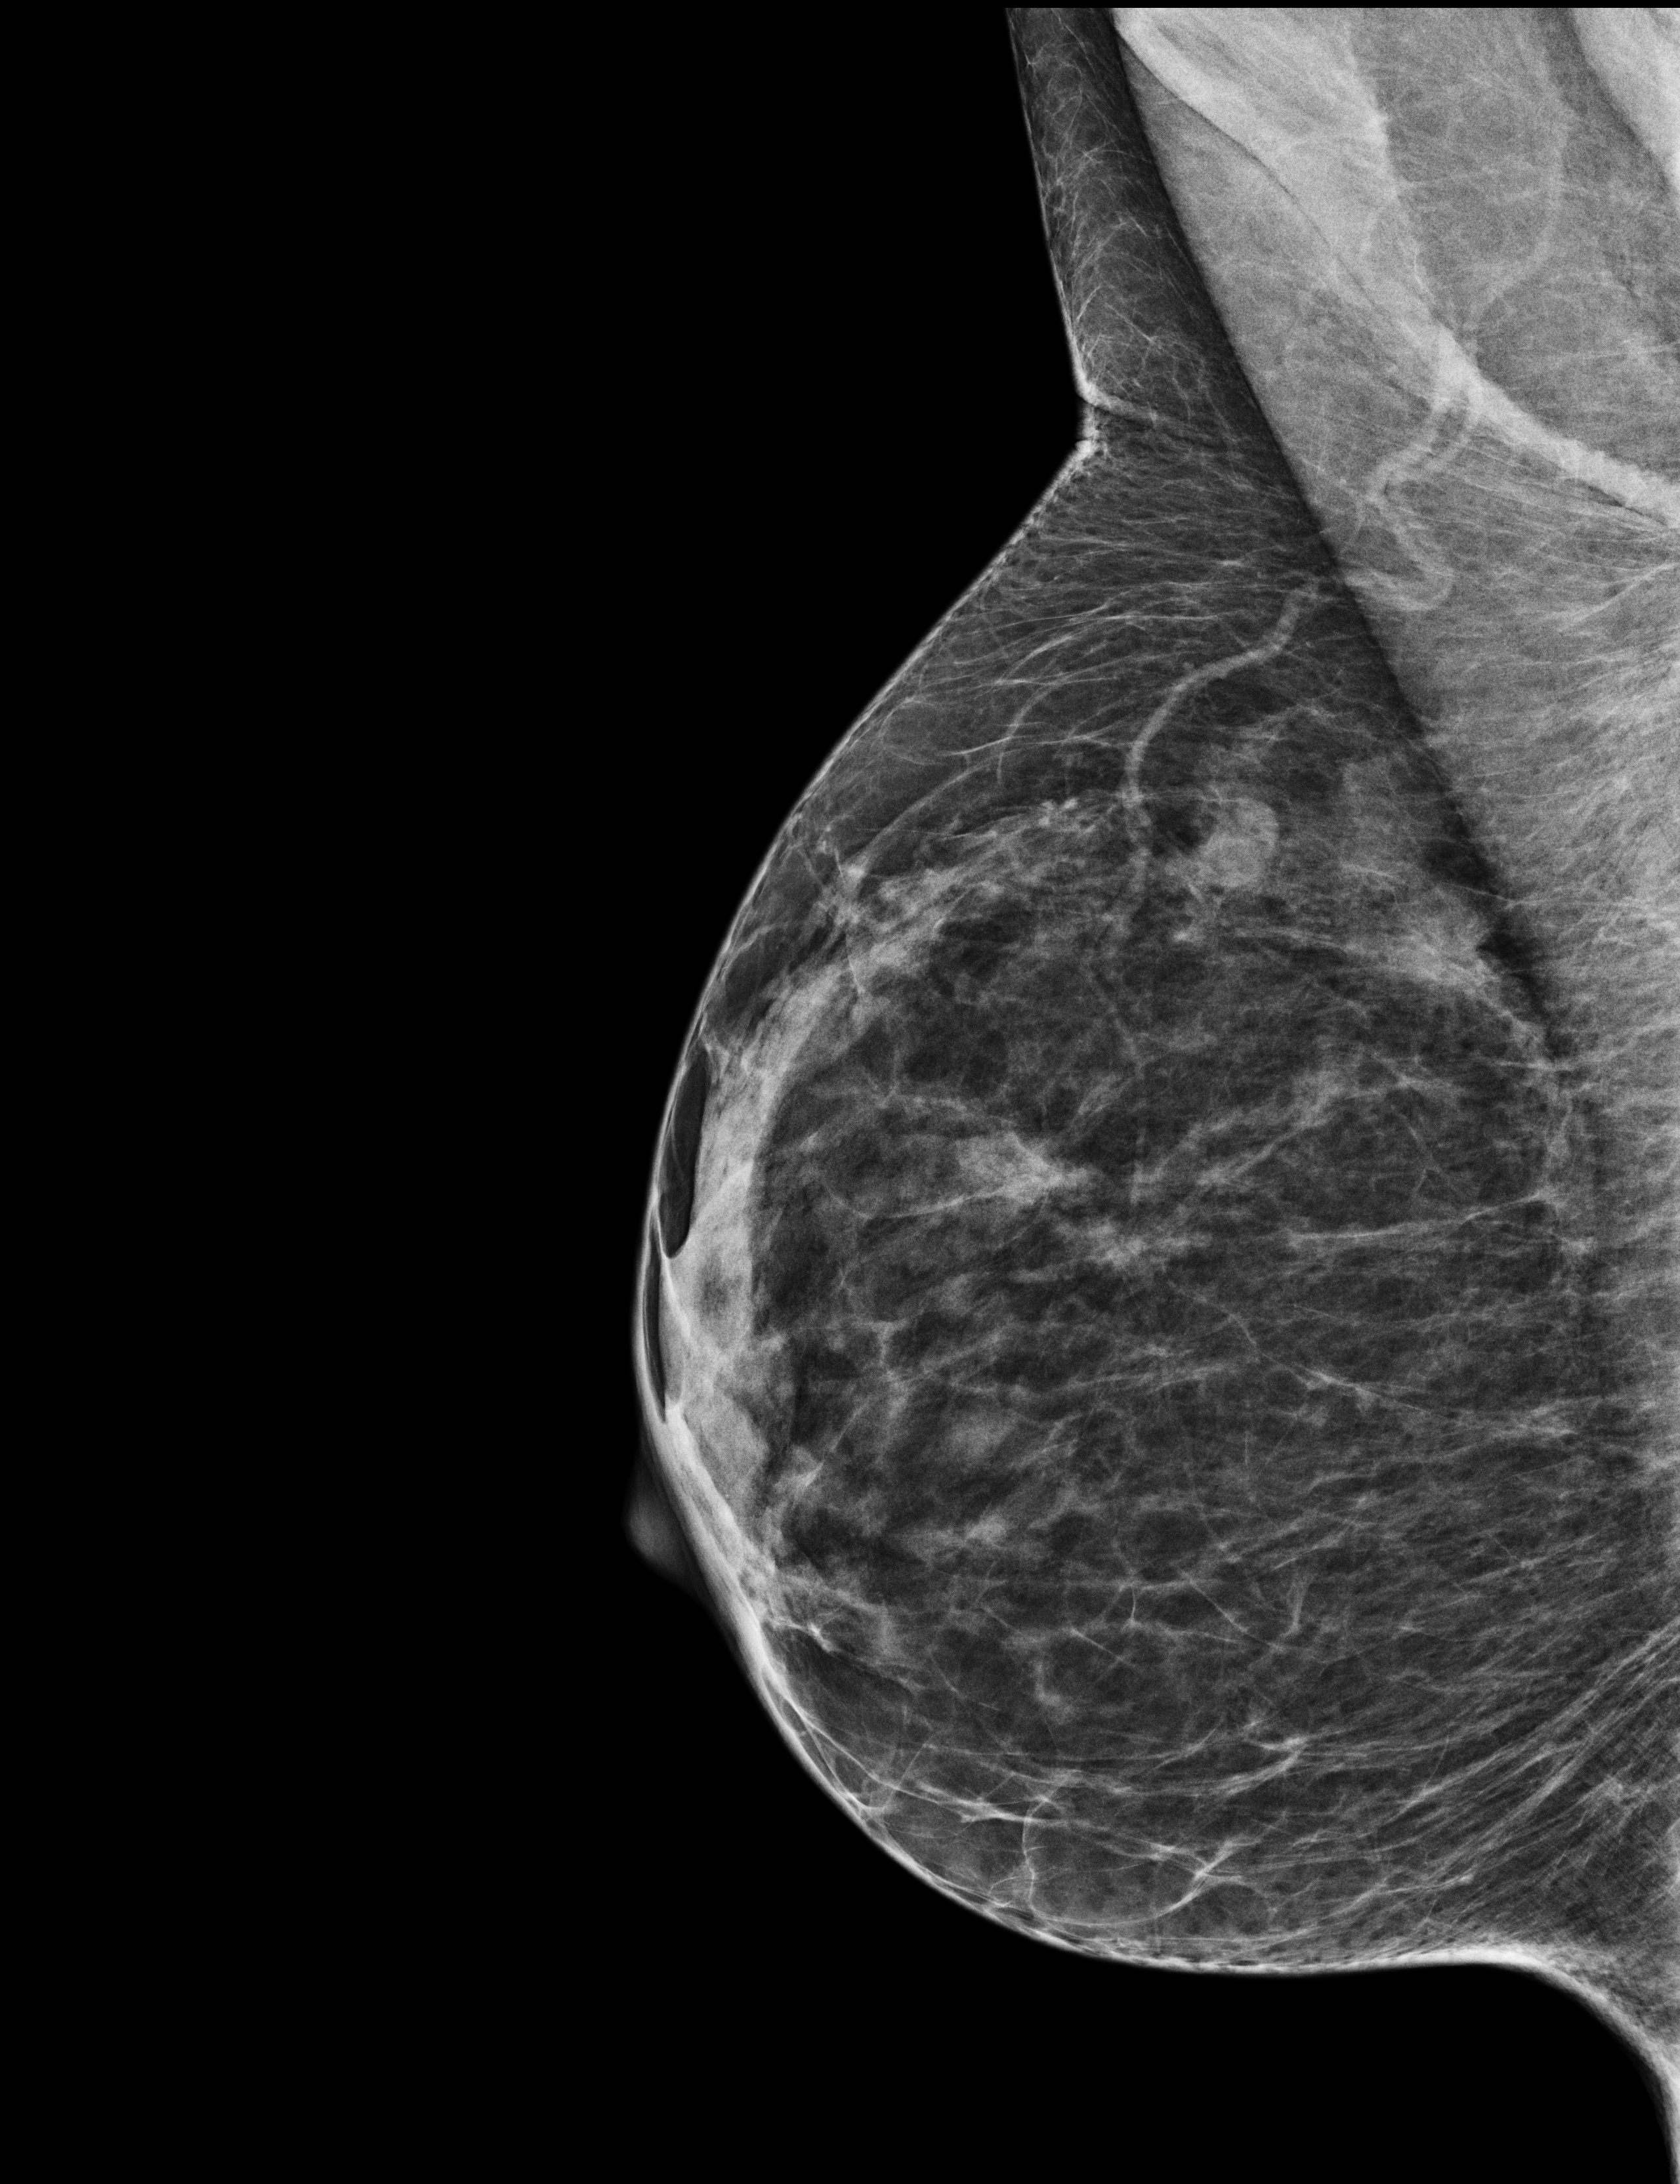
Diagnostic work-up study.
Image type: full-field digital mammogram. Breast: right. Projection: mediolateral oblique (MLO) view.